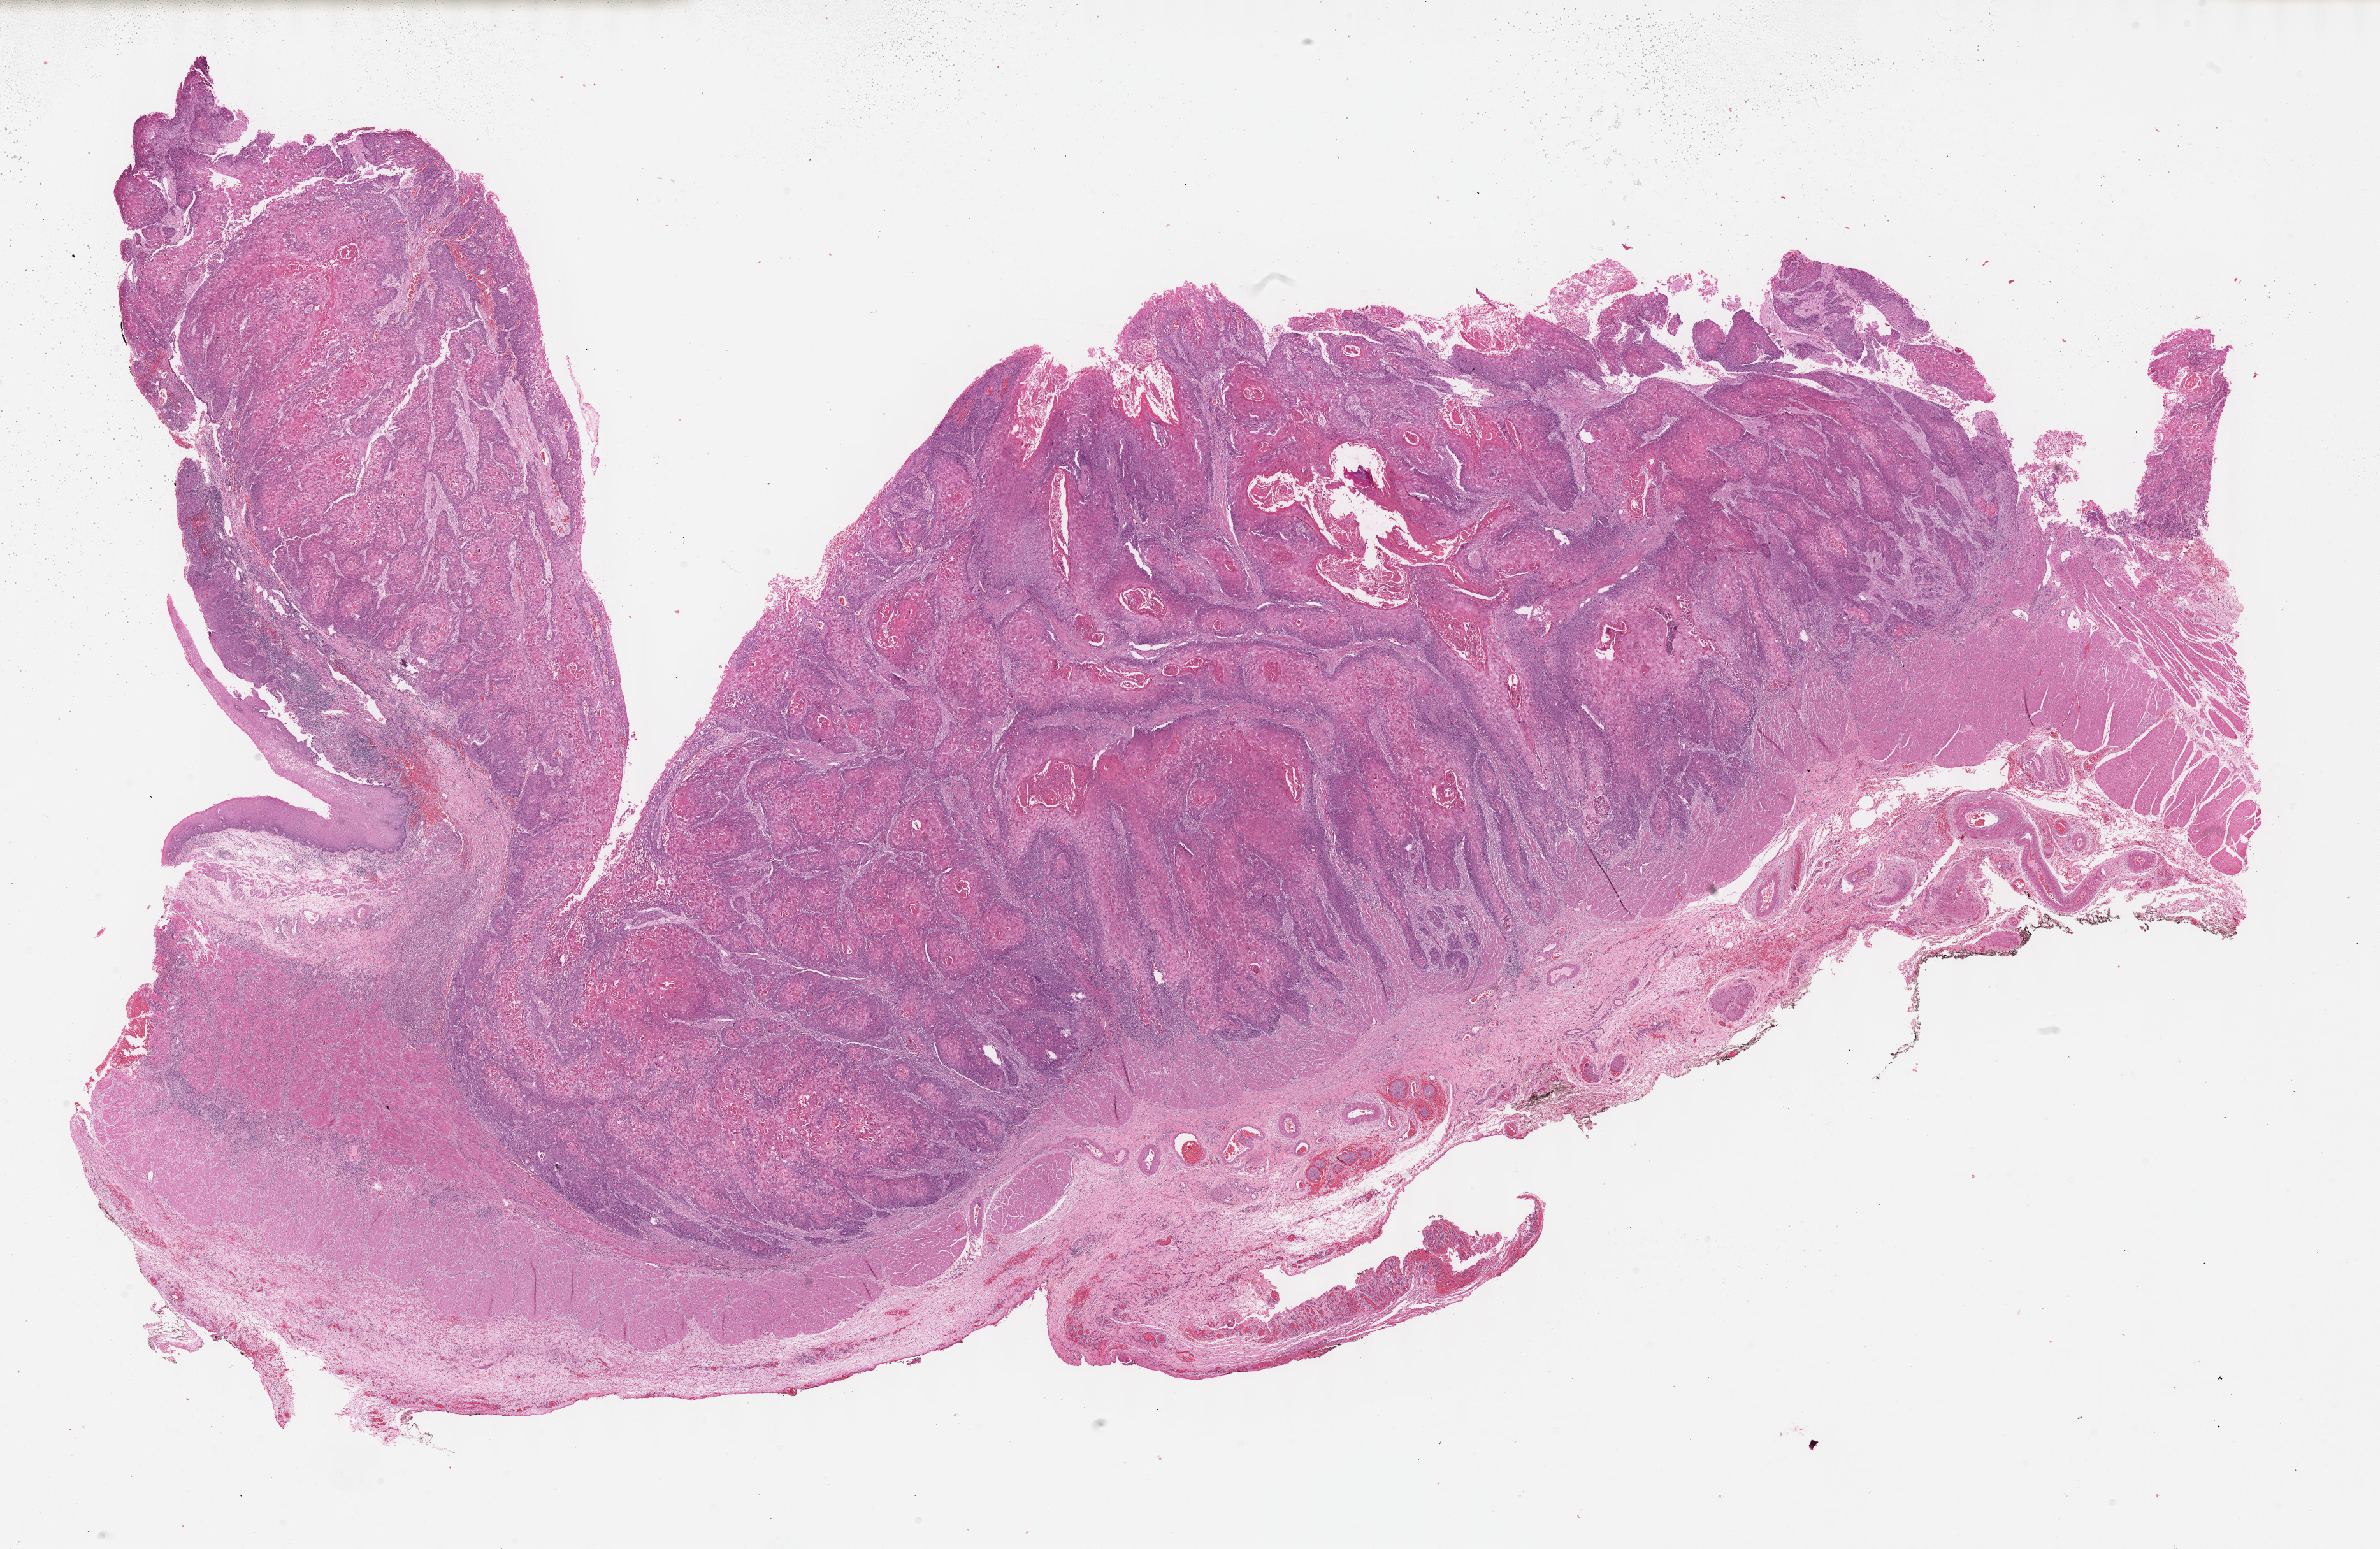
Whole-slide histology image, Hematoxylin and eosin (H&E) stained, low-resolution overview of the scanned area, about 30.2 x 19.6 mm. Formalin-fixed paraffin-embedded (FFPE) diagnostic section. Esophagus, primary tumour sample. Female, age 63 years at initial diagnosis. Histologic grade: G2 (moderately differentiated).
AJCC pathologic stage: IIA (7th edition). Histologic diagnosis: Squamous cell carcinoma, NOS (middle third of esophagus).